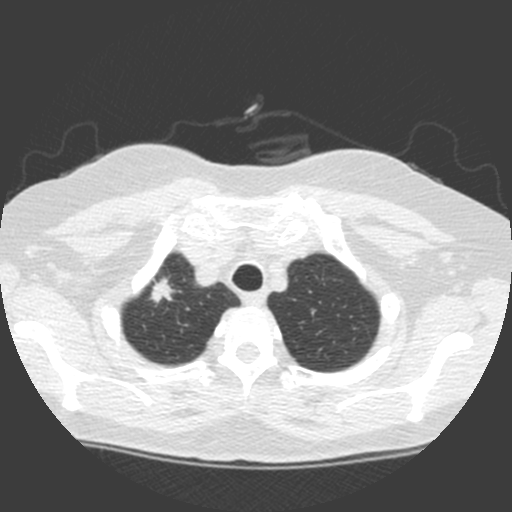
Low-dose screening chest CT, one axial slice; position 141 of 155 along the scan axis; lung window (W 1500 / L -600 HU); 2 mm slice thickness; 512 × 512 image matrix, field of view 314 × 314 mm.
Annotated regions visible in this slice (manually delineated by an expert):
- lesion 1 (tumor, upper lobe of right lung): bounding box (x1, y1, x2, y2) in pixels: (150, 277, 175, 303)